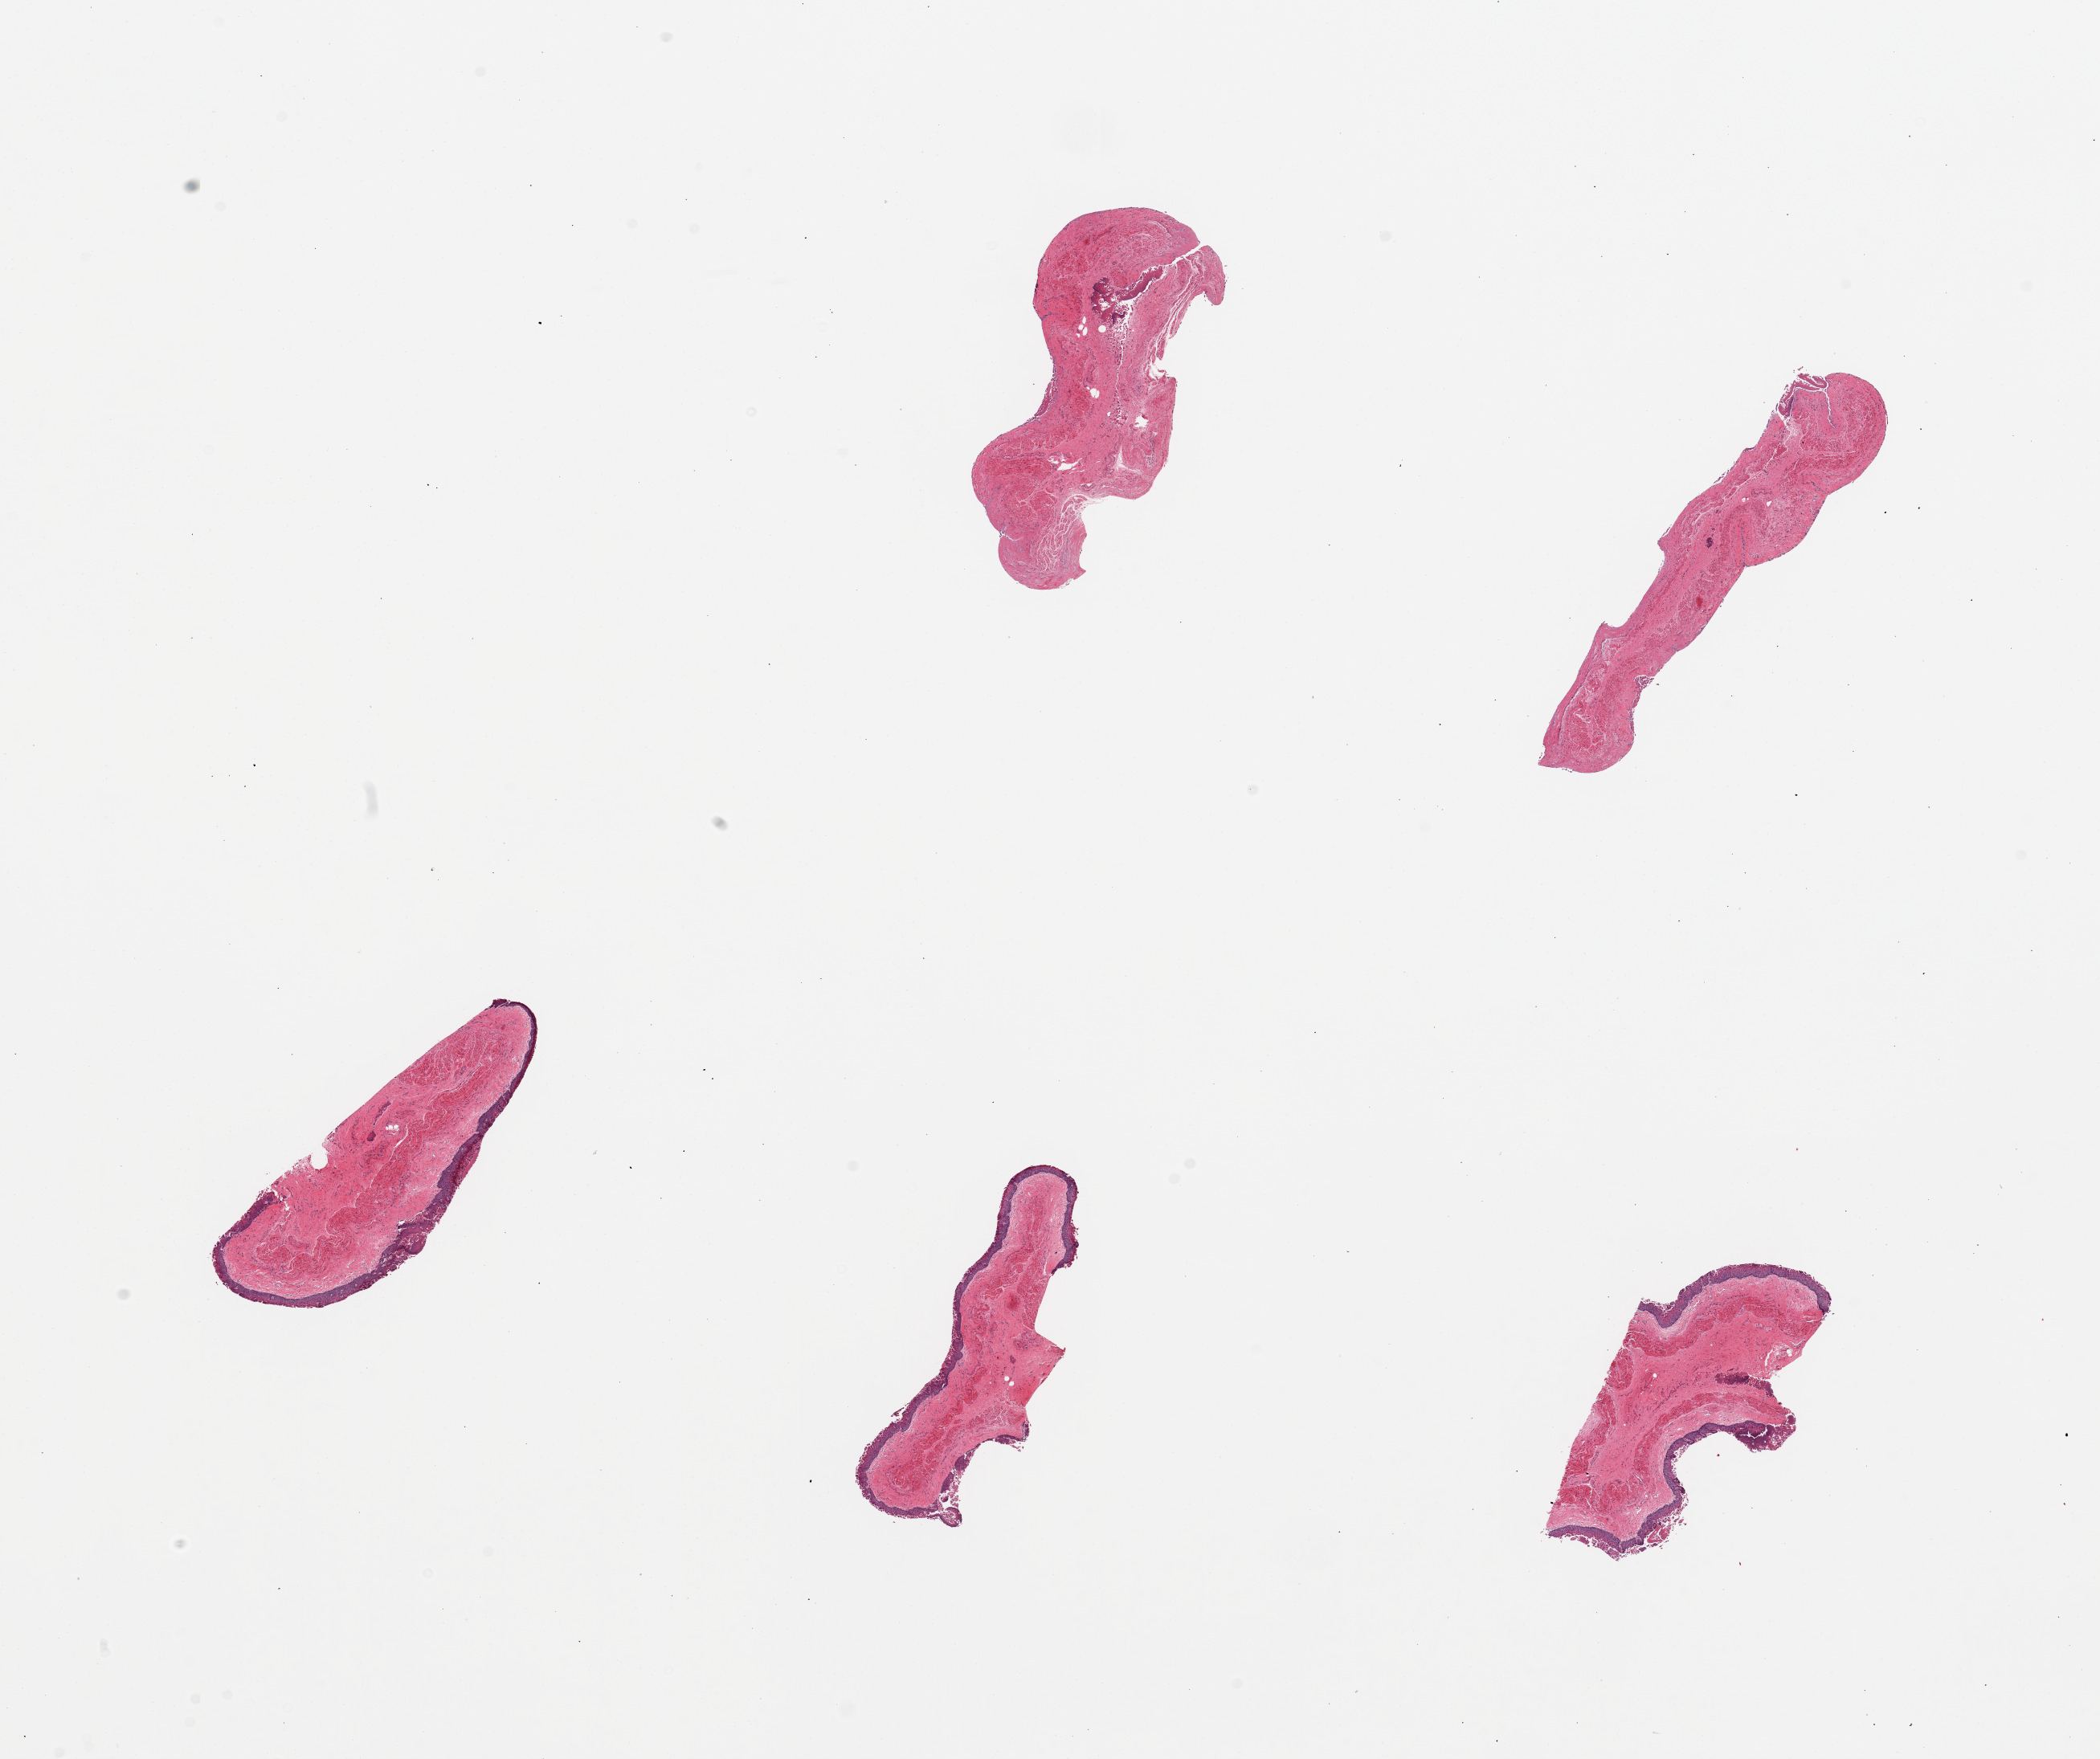
H&E whole-slide image — shown as a low-resolution overview of the whole scanned area (about 20.7 x 17.3 mm). PAXgene-fixed, paraffin-embedded tissue. Target tissue: esophageal mucous membrane. Tissue donor sample. Female donor.
* pathologist's review note for this sample: 5 pieces; 3 have fragmented epithelium; 2 have no epithelium